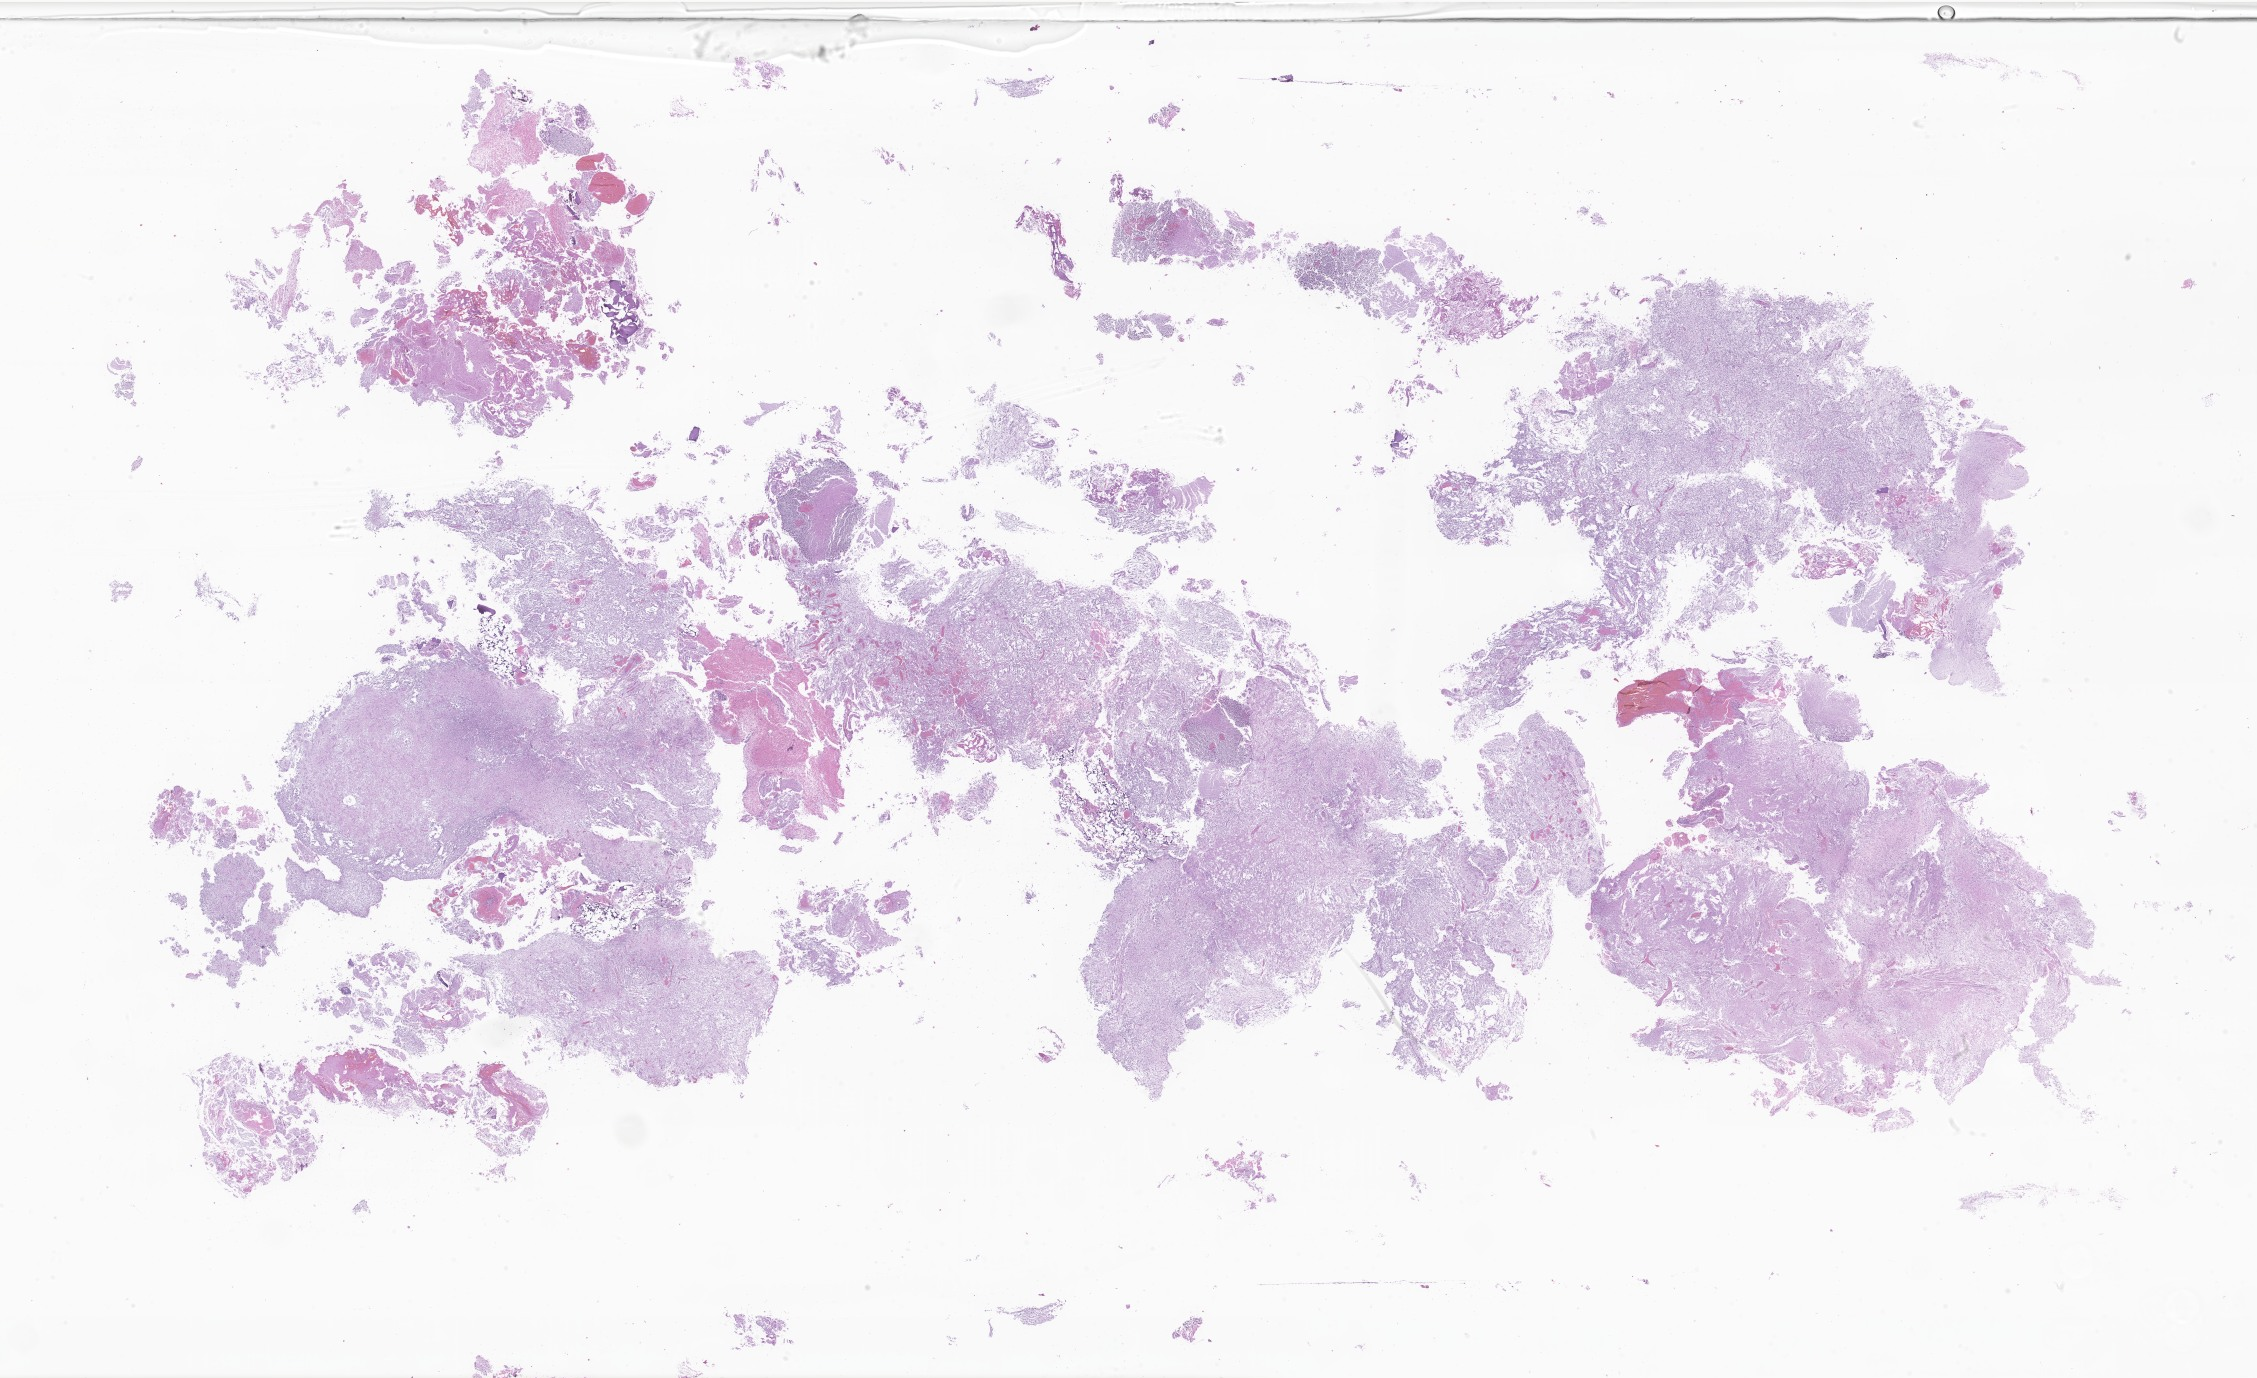
Haematoxylin and eosin whole-slide image of tumor tissue from the brain — a low-resolution overview of the entire scanned area, about 38.1 x 23.2 mm; formalin-fixed, paraffin-embedded (FFPE) tissue. Female patient, age 176 months (14 years 8 months).
- recorded diagnosis: Pilocytic astrocytoma